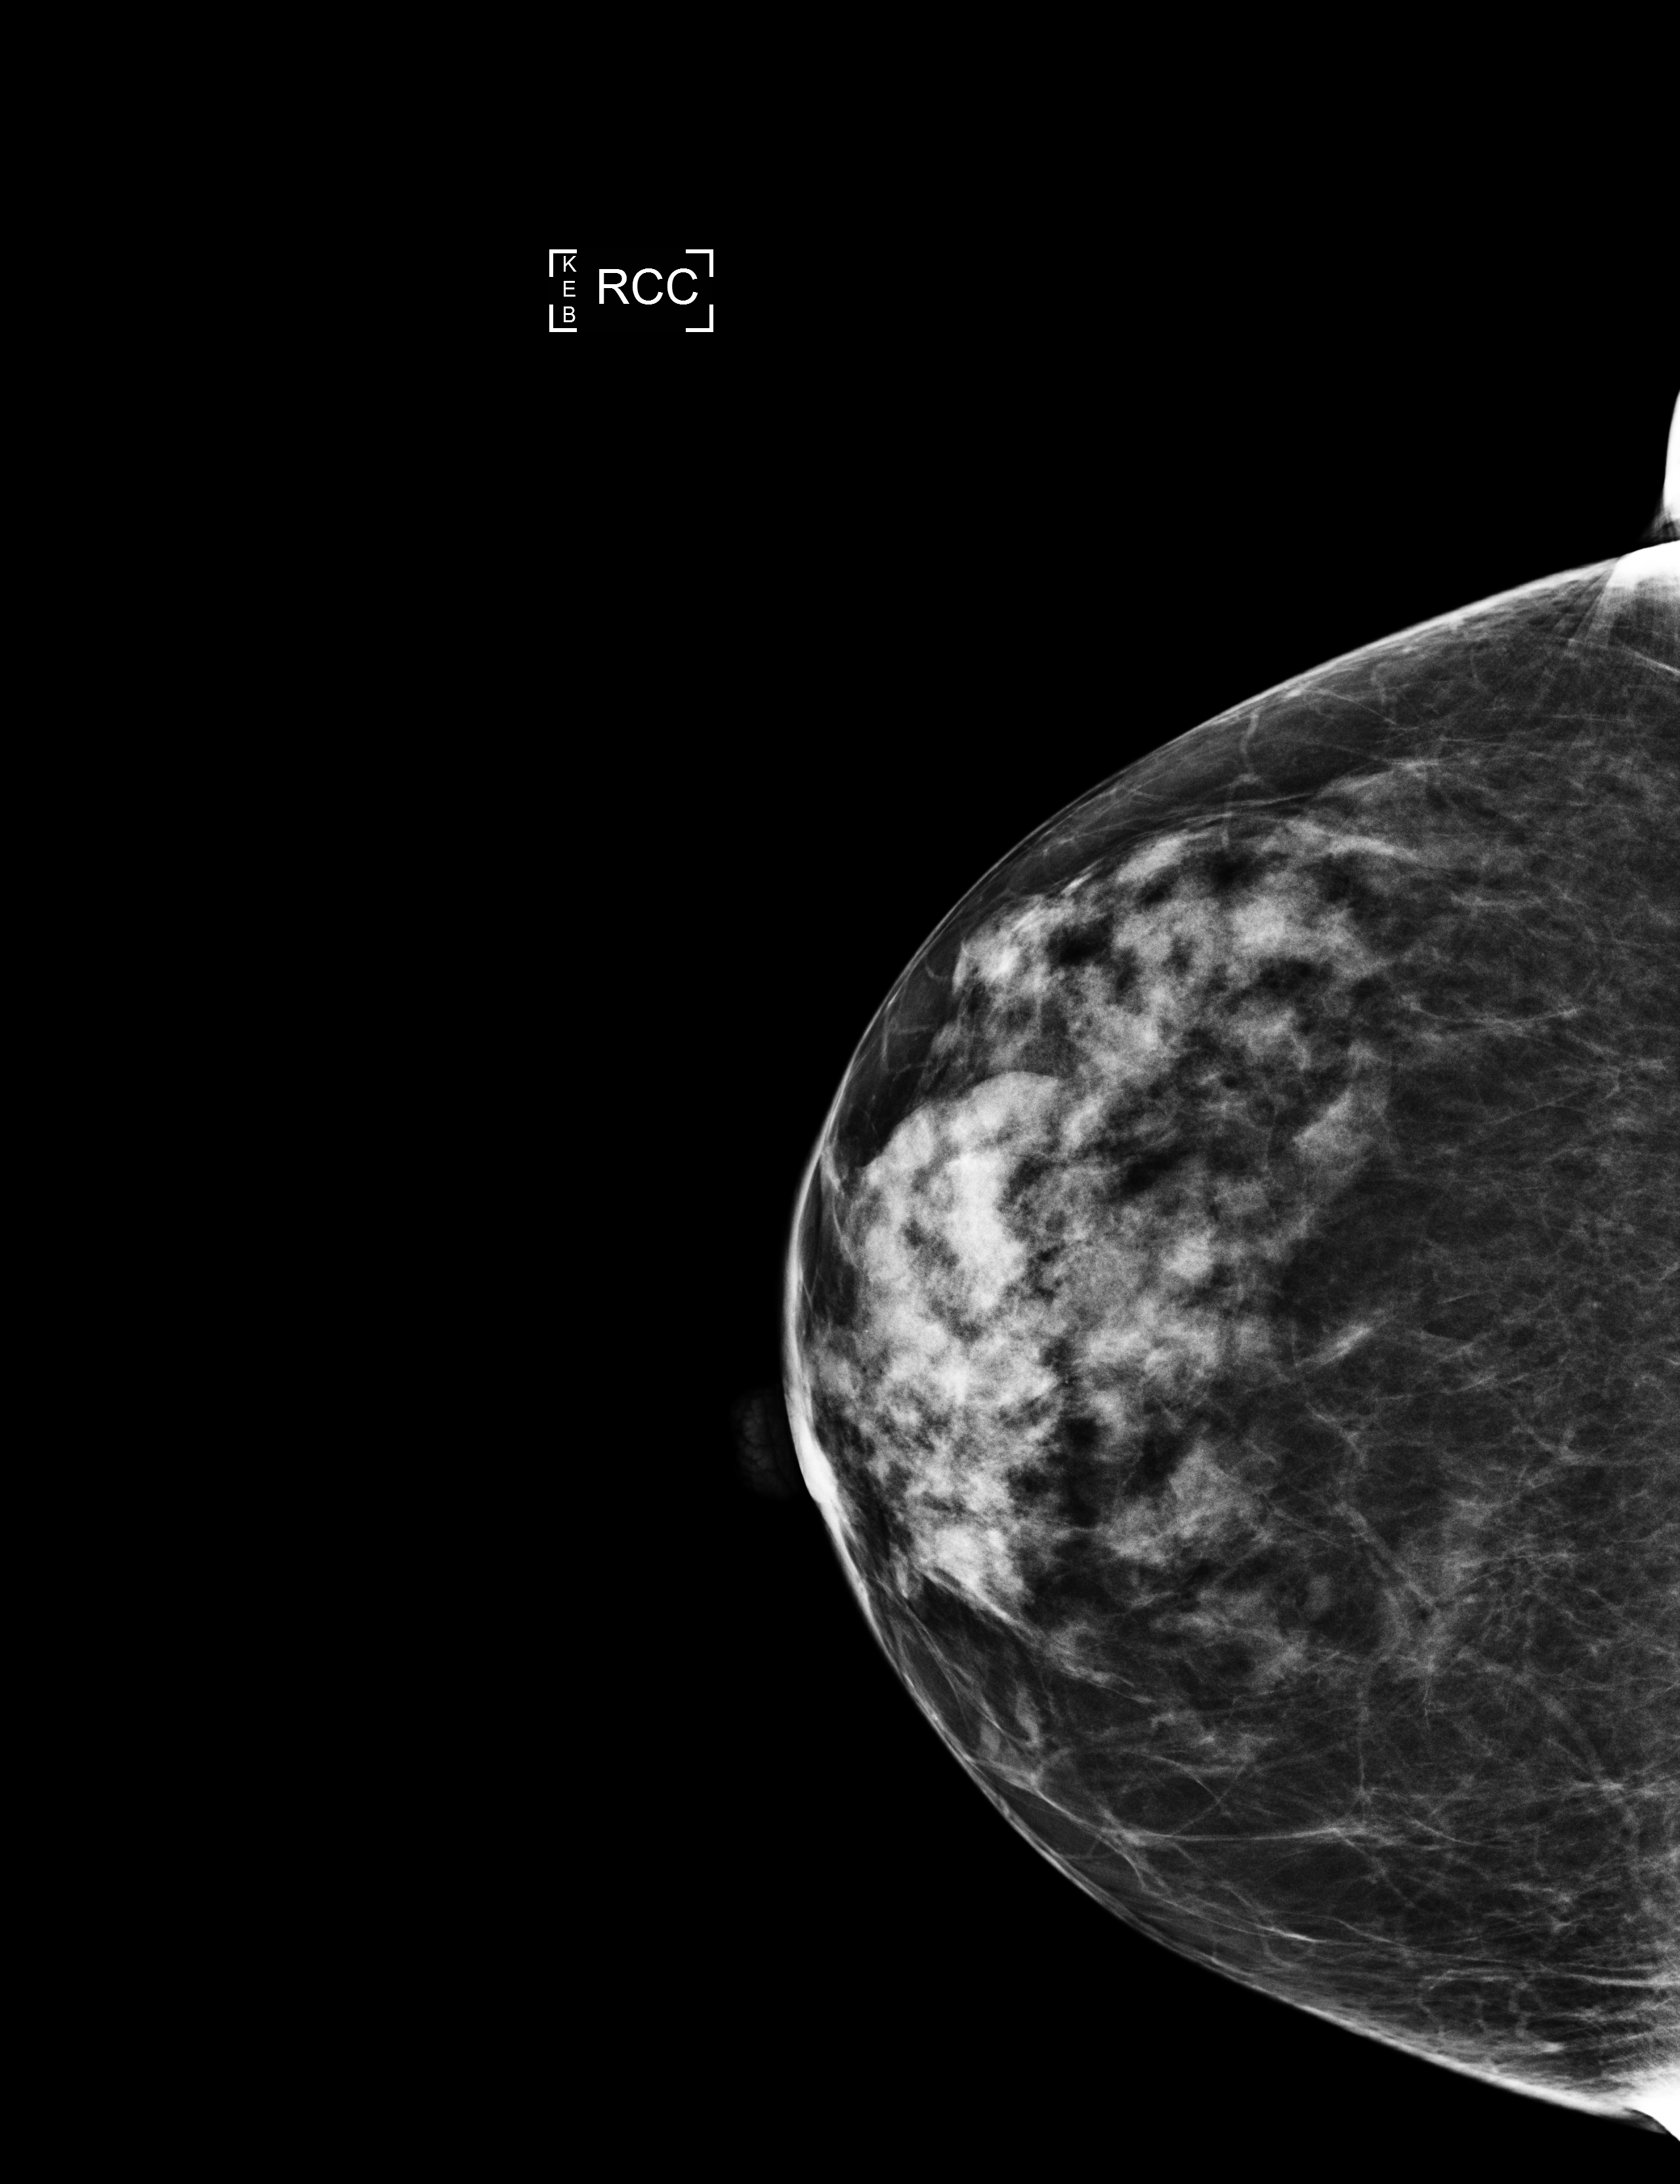
Digital mammogram (FFDM), right breast, craniocaudal (CC) view, annual screening mammography examination. Patient: female, 72 years.
- BI-RADS breast density category at the screening exam (both breasts, scale 1–4): 3
- final BI-RADS category for the screening round (tomosynthesis exam, both breasts): category 1
- recall: no recall after this screen